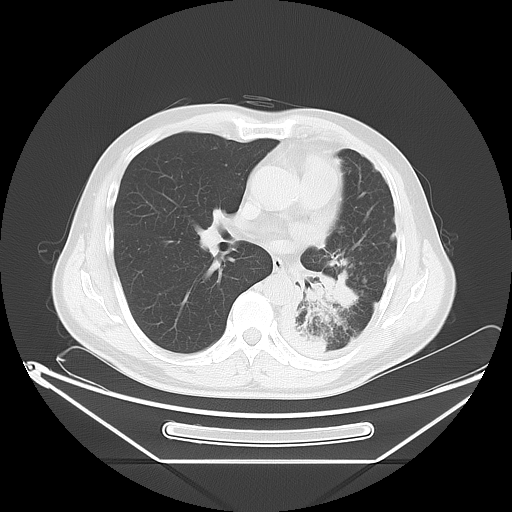
Chest CT, one axial slice. Slice 33 of 63 in the series (ordered by position). Reconstruction kernel LUNG. Lung window (W 1500 / L -600 HU). 512 × 512 image matrix. Male patient, age 60 years. Case-level facts recorded for this patient, not image findings: clinical TNM (as recorded): T4 N1 M1.
Structures marked on this image (bounding box drawn by a radiologist):
- lung tumour (recorded histology: adenocarcinoma): bounding box [x1, y1, x2, y2] px = [290, 256, 358, 329]